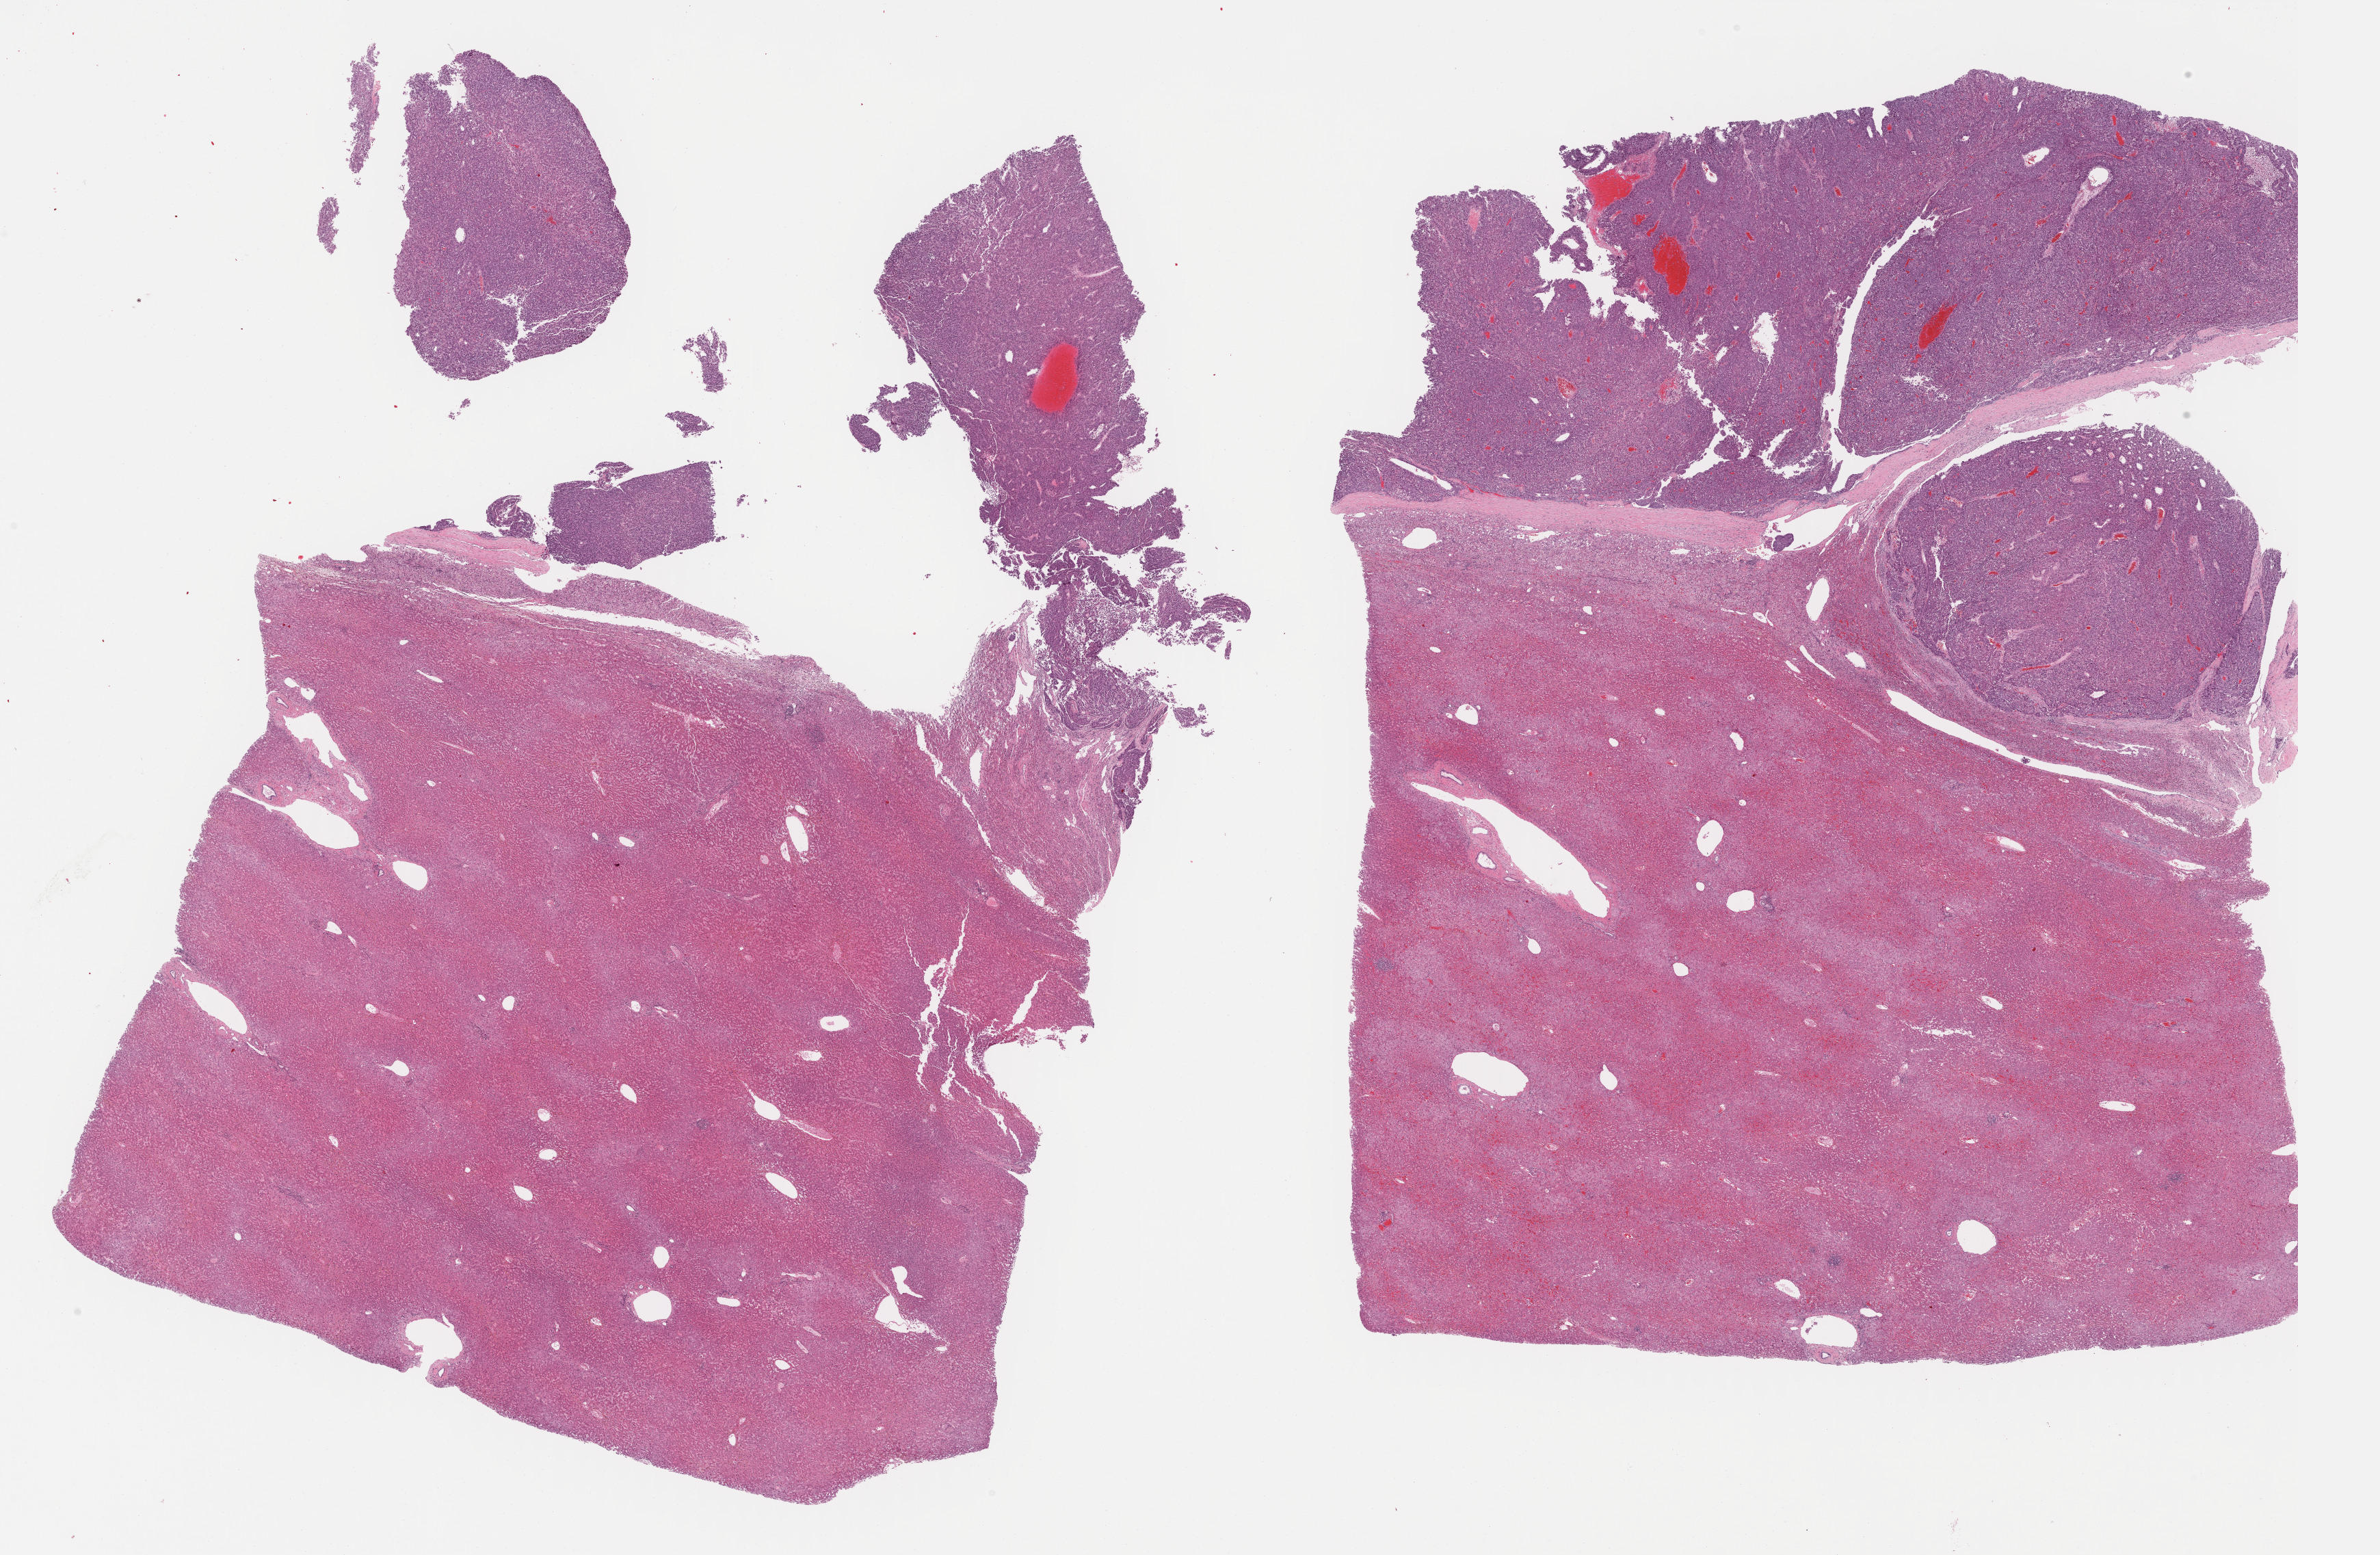
Digitized H&E tissue section (whole slide) — a low-resolution overview of the entire scanned area, about 28.2 x 18.4 mm, FFPE section, sample: primary tumour, liver. Female patient; age at initial diagnosis 71 years.
Diagnosis: Hepatocellular carcinoma, NOS.